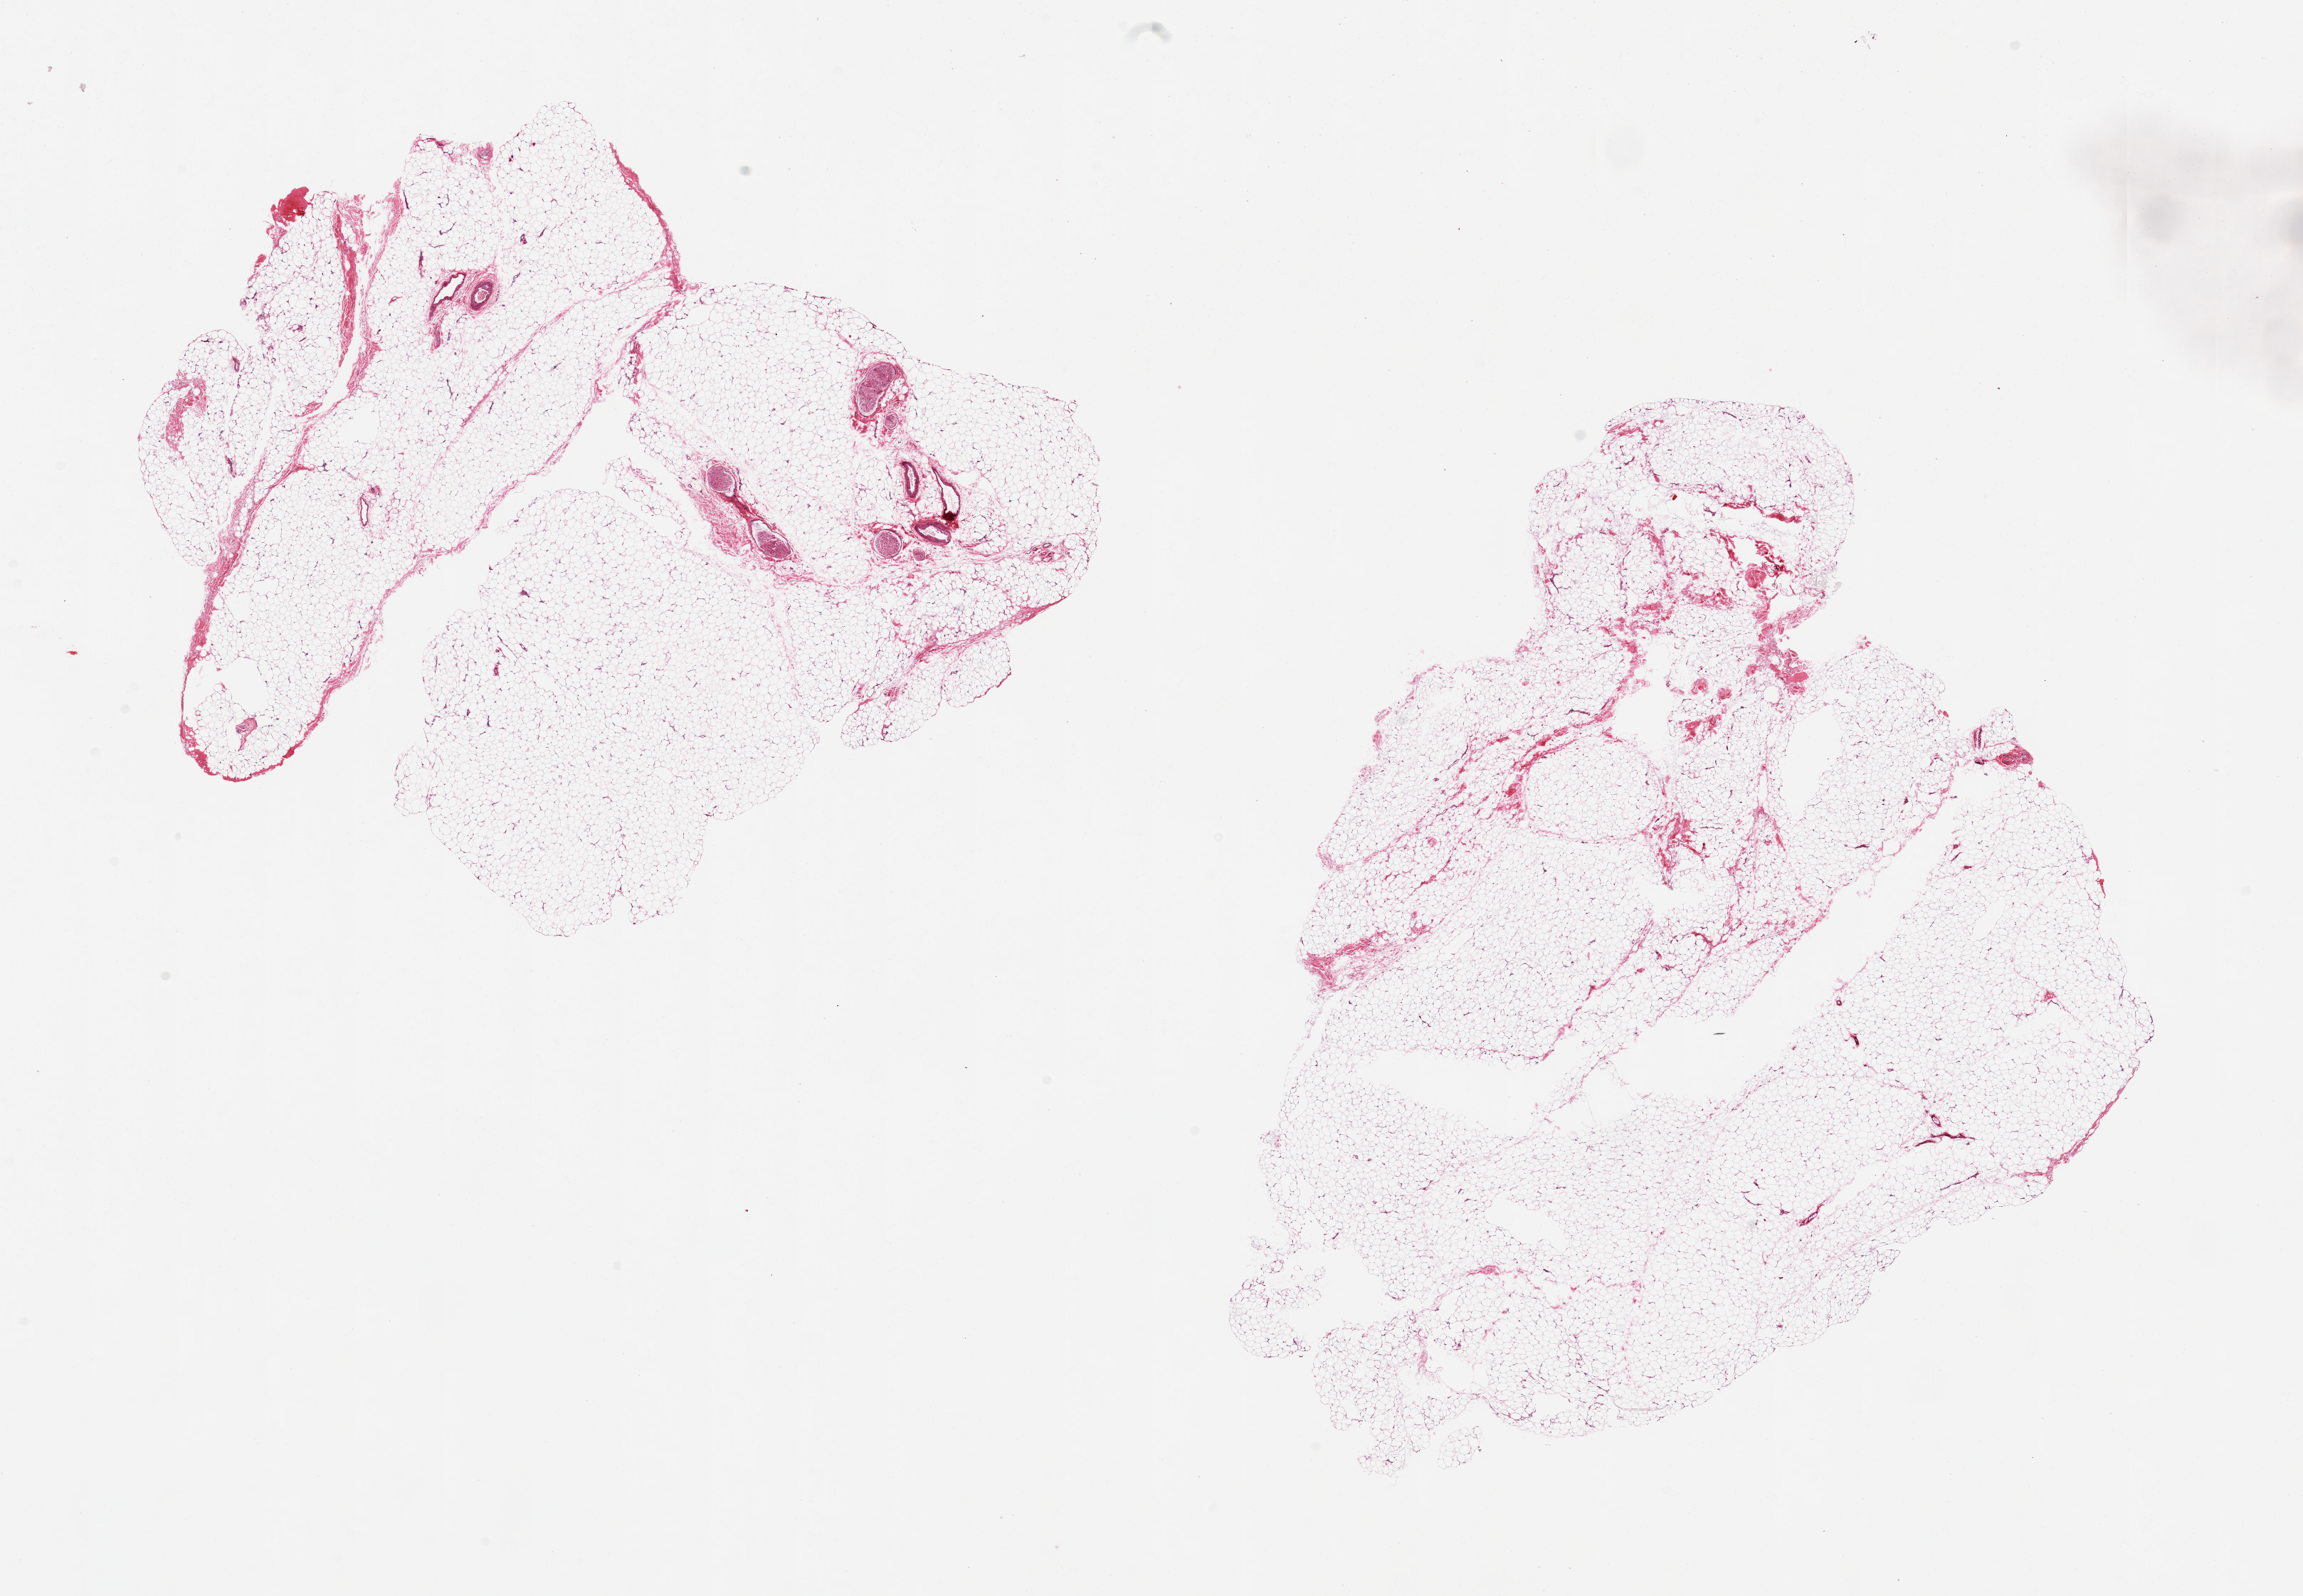
Digitized H&E-stained section, a low-resolution overview of the entire scanned area, about 25.6 x 17.7 mm, PAXgene-fixed paraffin-embedded (PFPE) section, sampled site (target tissue): adipose tissue, donor tissue sample. Donor sex: female.
- review note (as recorded): 2 pieces